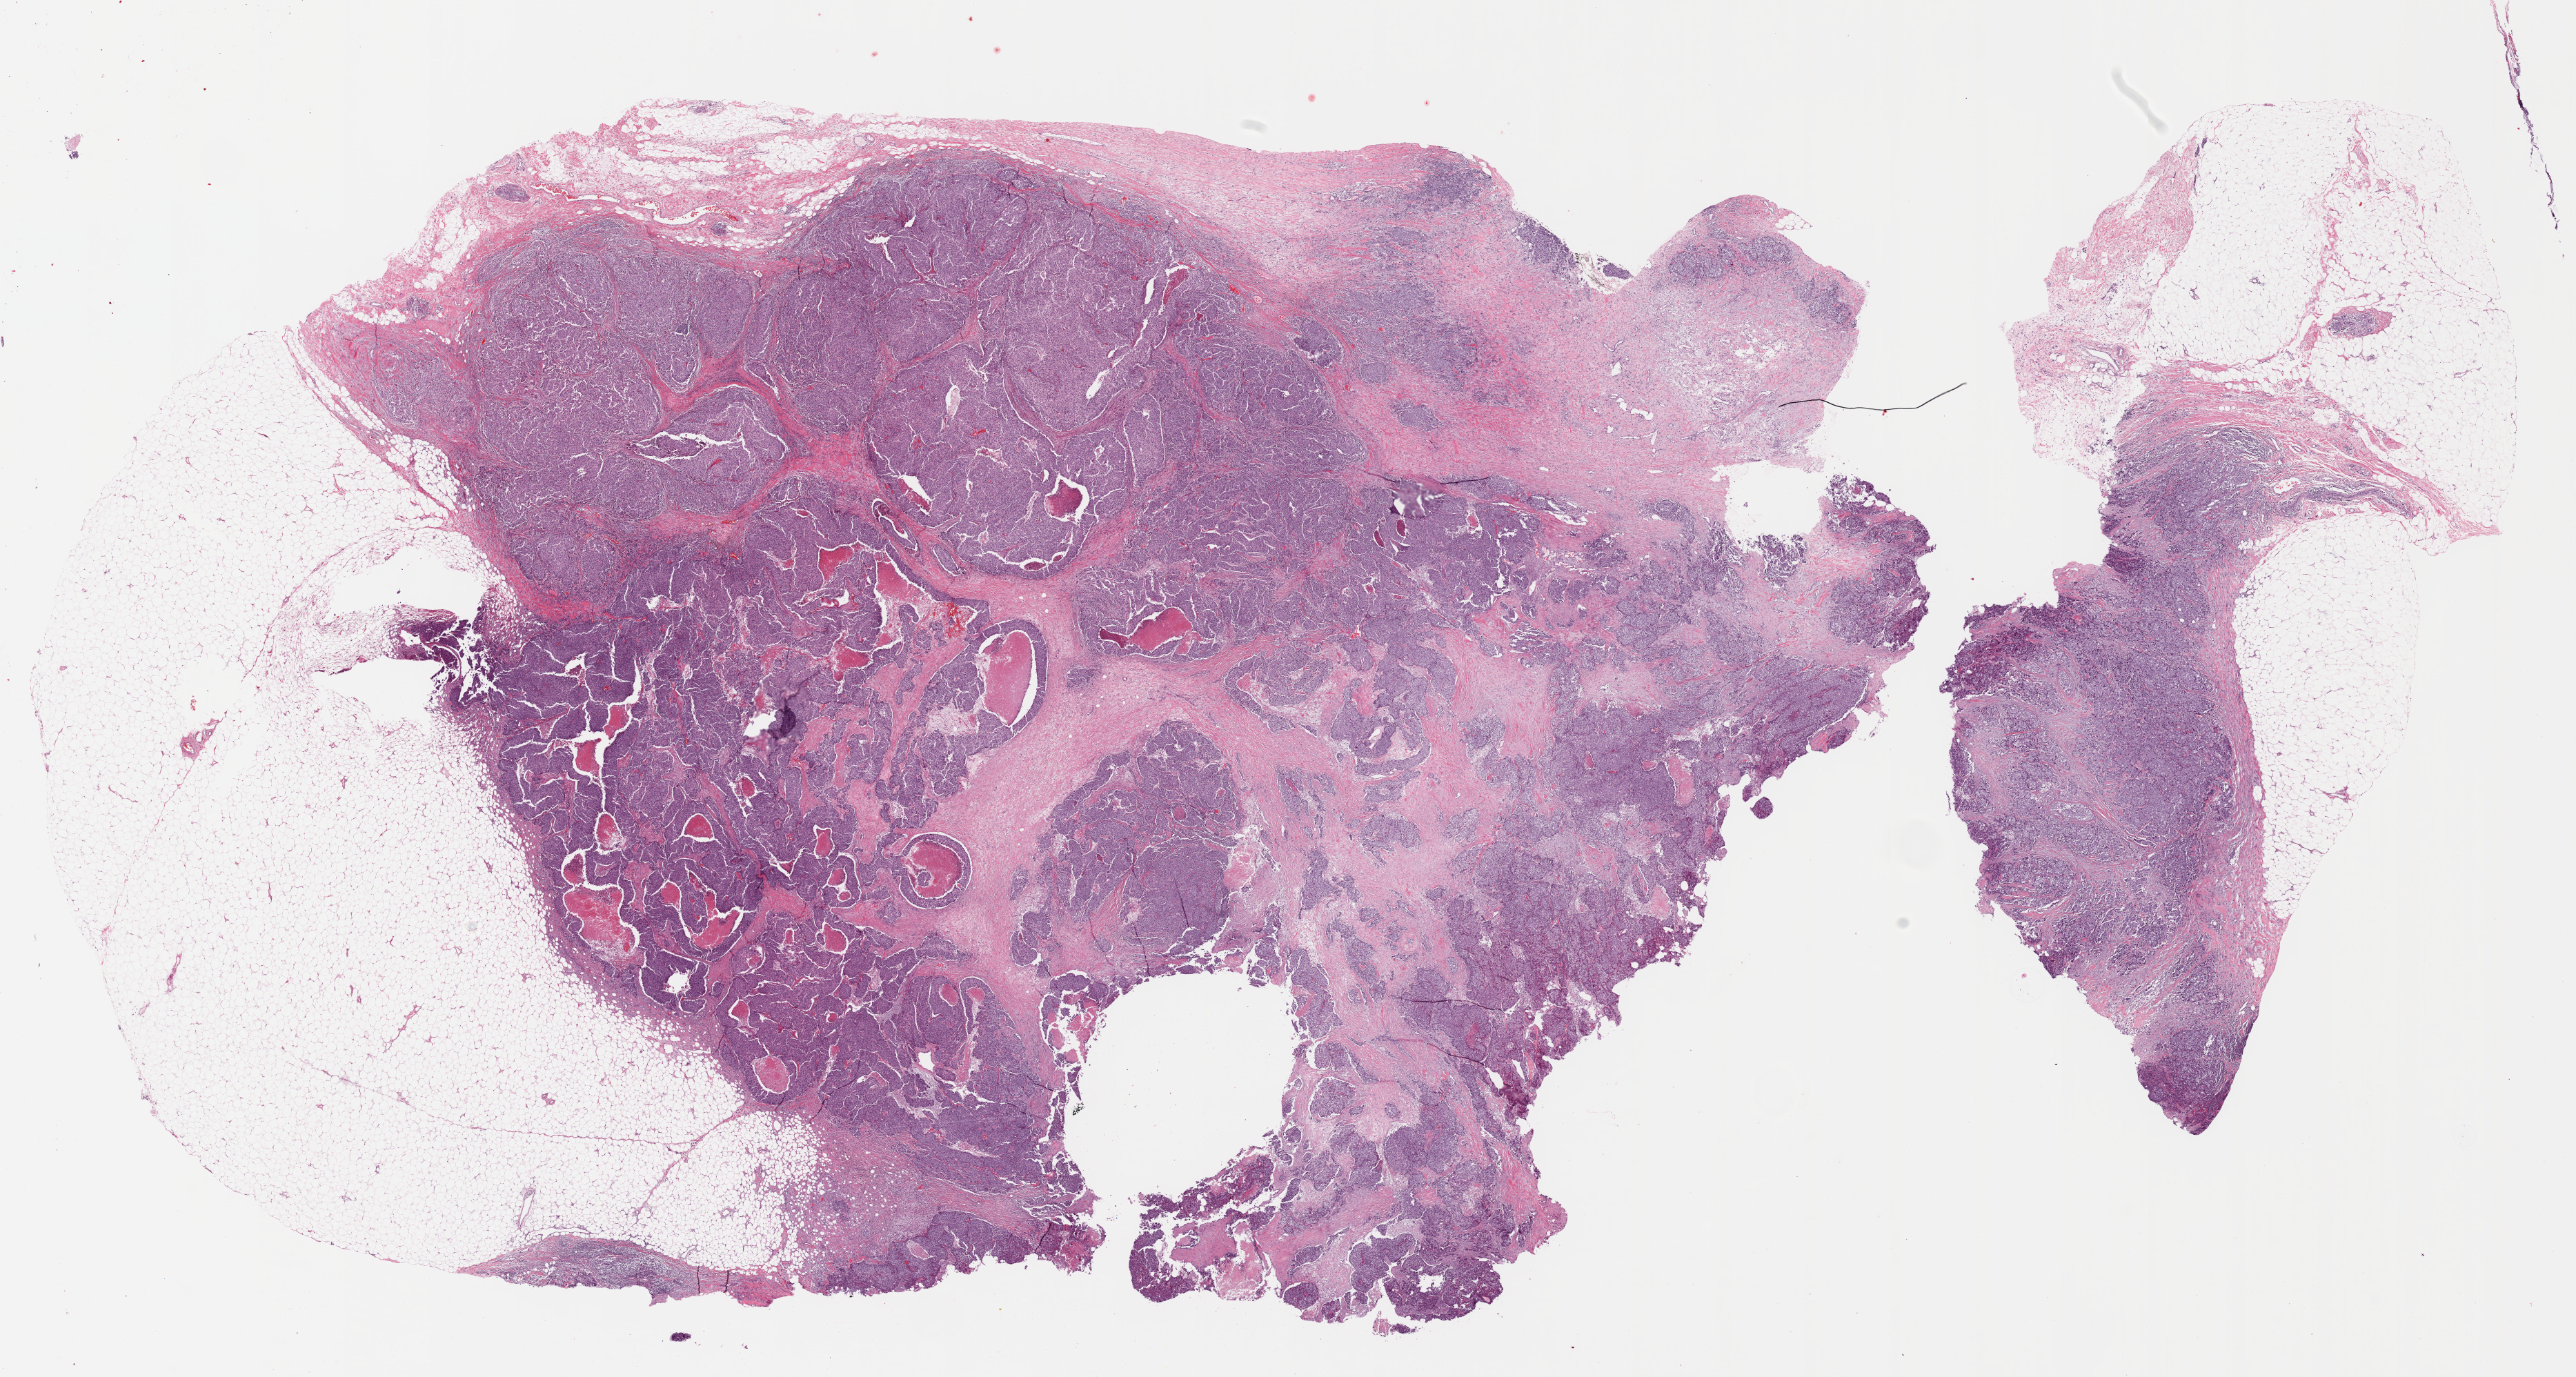
Whole-slide histology image, Hematoxylin and eosin (H&E) stained — low-resolution overview of the scanned area, about 29.8 x 15.9 mm (acquisition: 20x scan), FFPE section, primary tumour sample from the breast. Female patient; age at initial diagnosis 69 years.
Laterality: right. AJCC pathologic stage: IIA. Pathologic diagnosis: Infiltrating duct carcinoma, NOS.